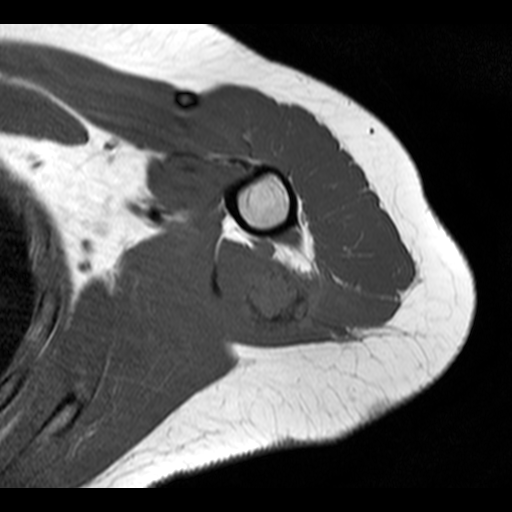
MRI of an extremity soft-tissue mass, one axial slice. Position 5 of 20 along the scan axis. 512 × 512 image matrix, field of view 150 × 150 mm. Female patient. Case-level facts recorded for this patient, not image findings: histological type: malignant fibrous histiocytoma; grade: low; site of the primary tumour: left arm.
Structures marked on this image (manually delineated by an expert):
- gross tumour volume (mass): bounding box (x1, y1, x2, y2) in pixels: (243, 246, 323, 334)